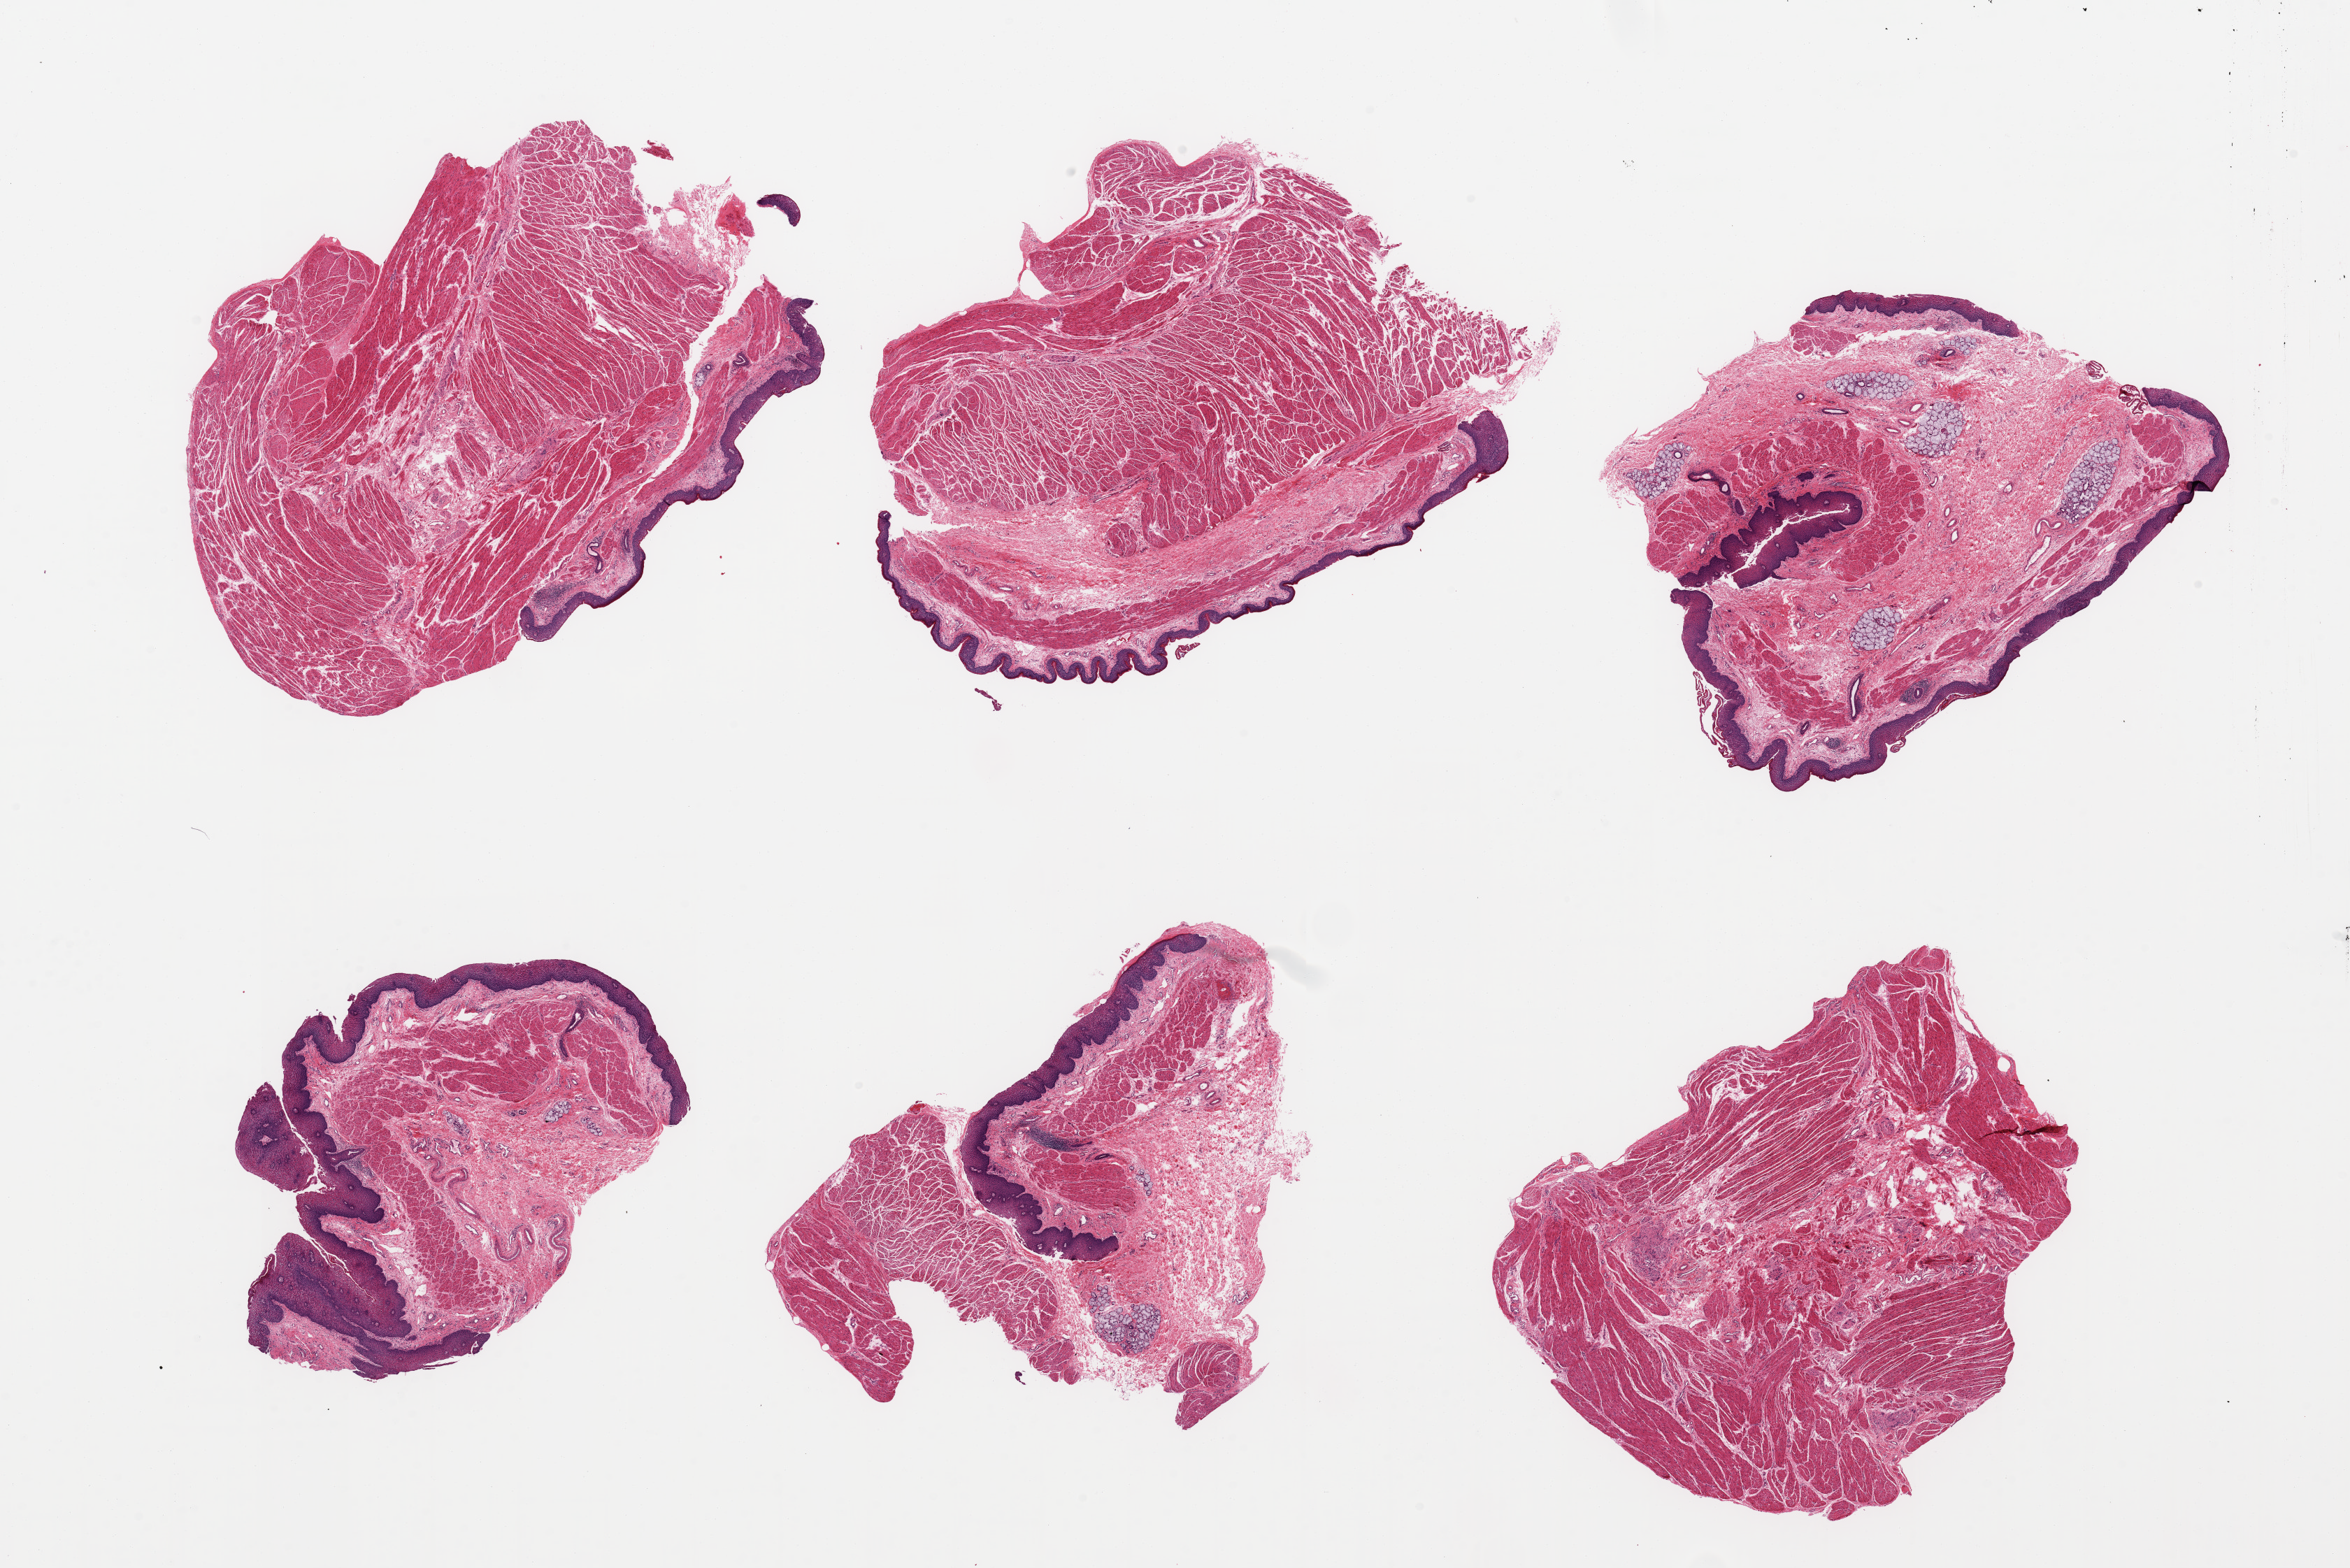
Digitized hematoxylin and eosin (H&E)-stained section — a low-resolution overview of the entire scanned area, about 26.6 x 17.7 mm; PAXgene-fixed paraffin-embedded (PFPE) section; target tissue: gastroesophageal junction; tissue donor sample. Male donor.
Pathologist's review note for this sample: 6 pieces, confirmed target muscularis, trace 'contaminant' mucosa.